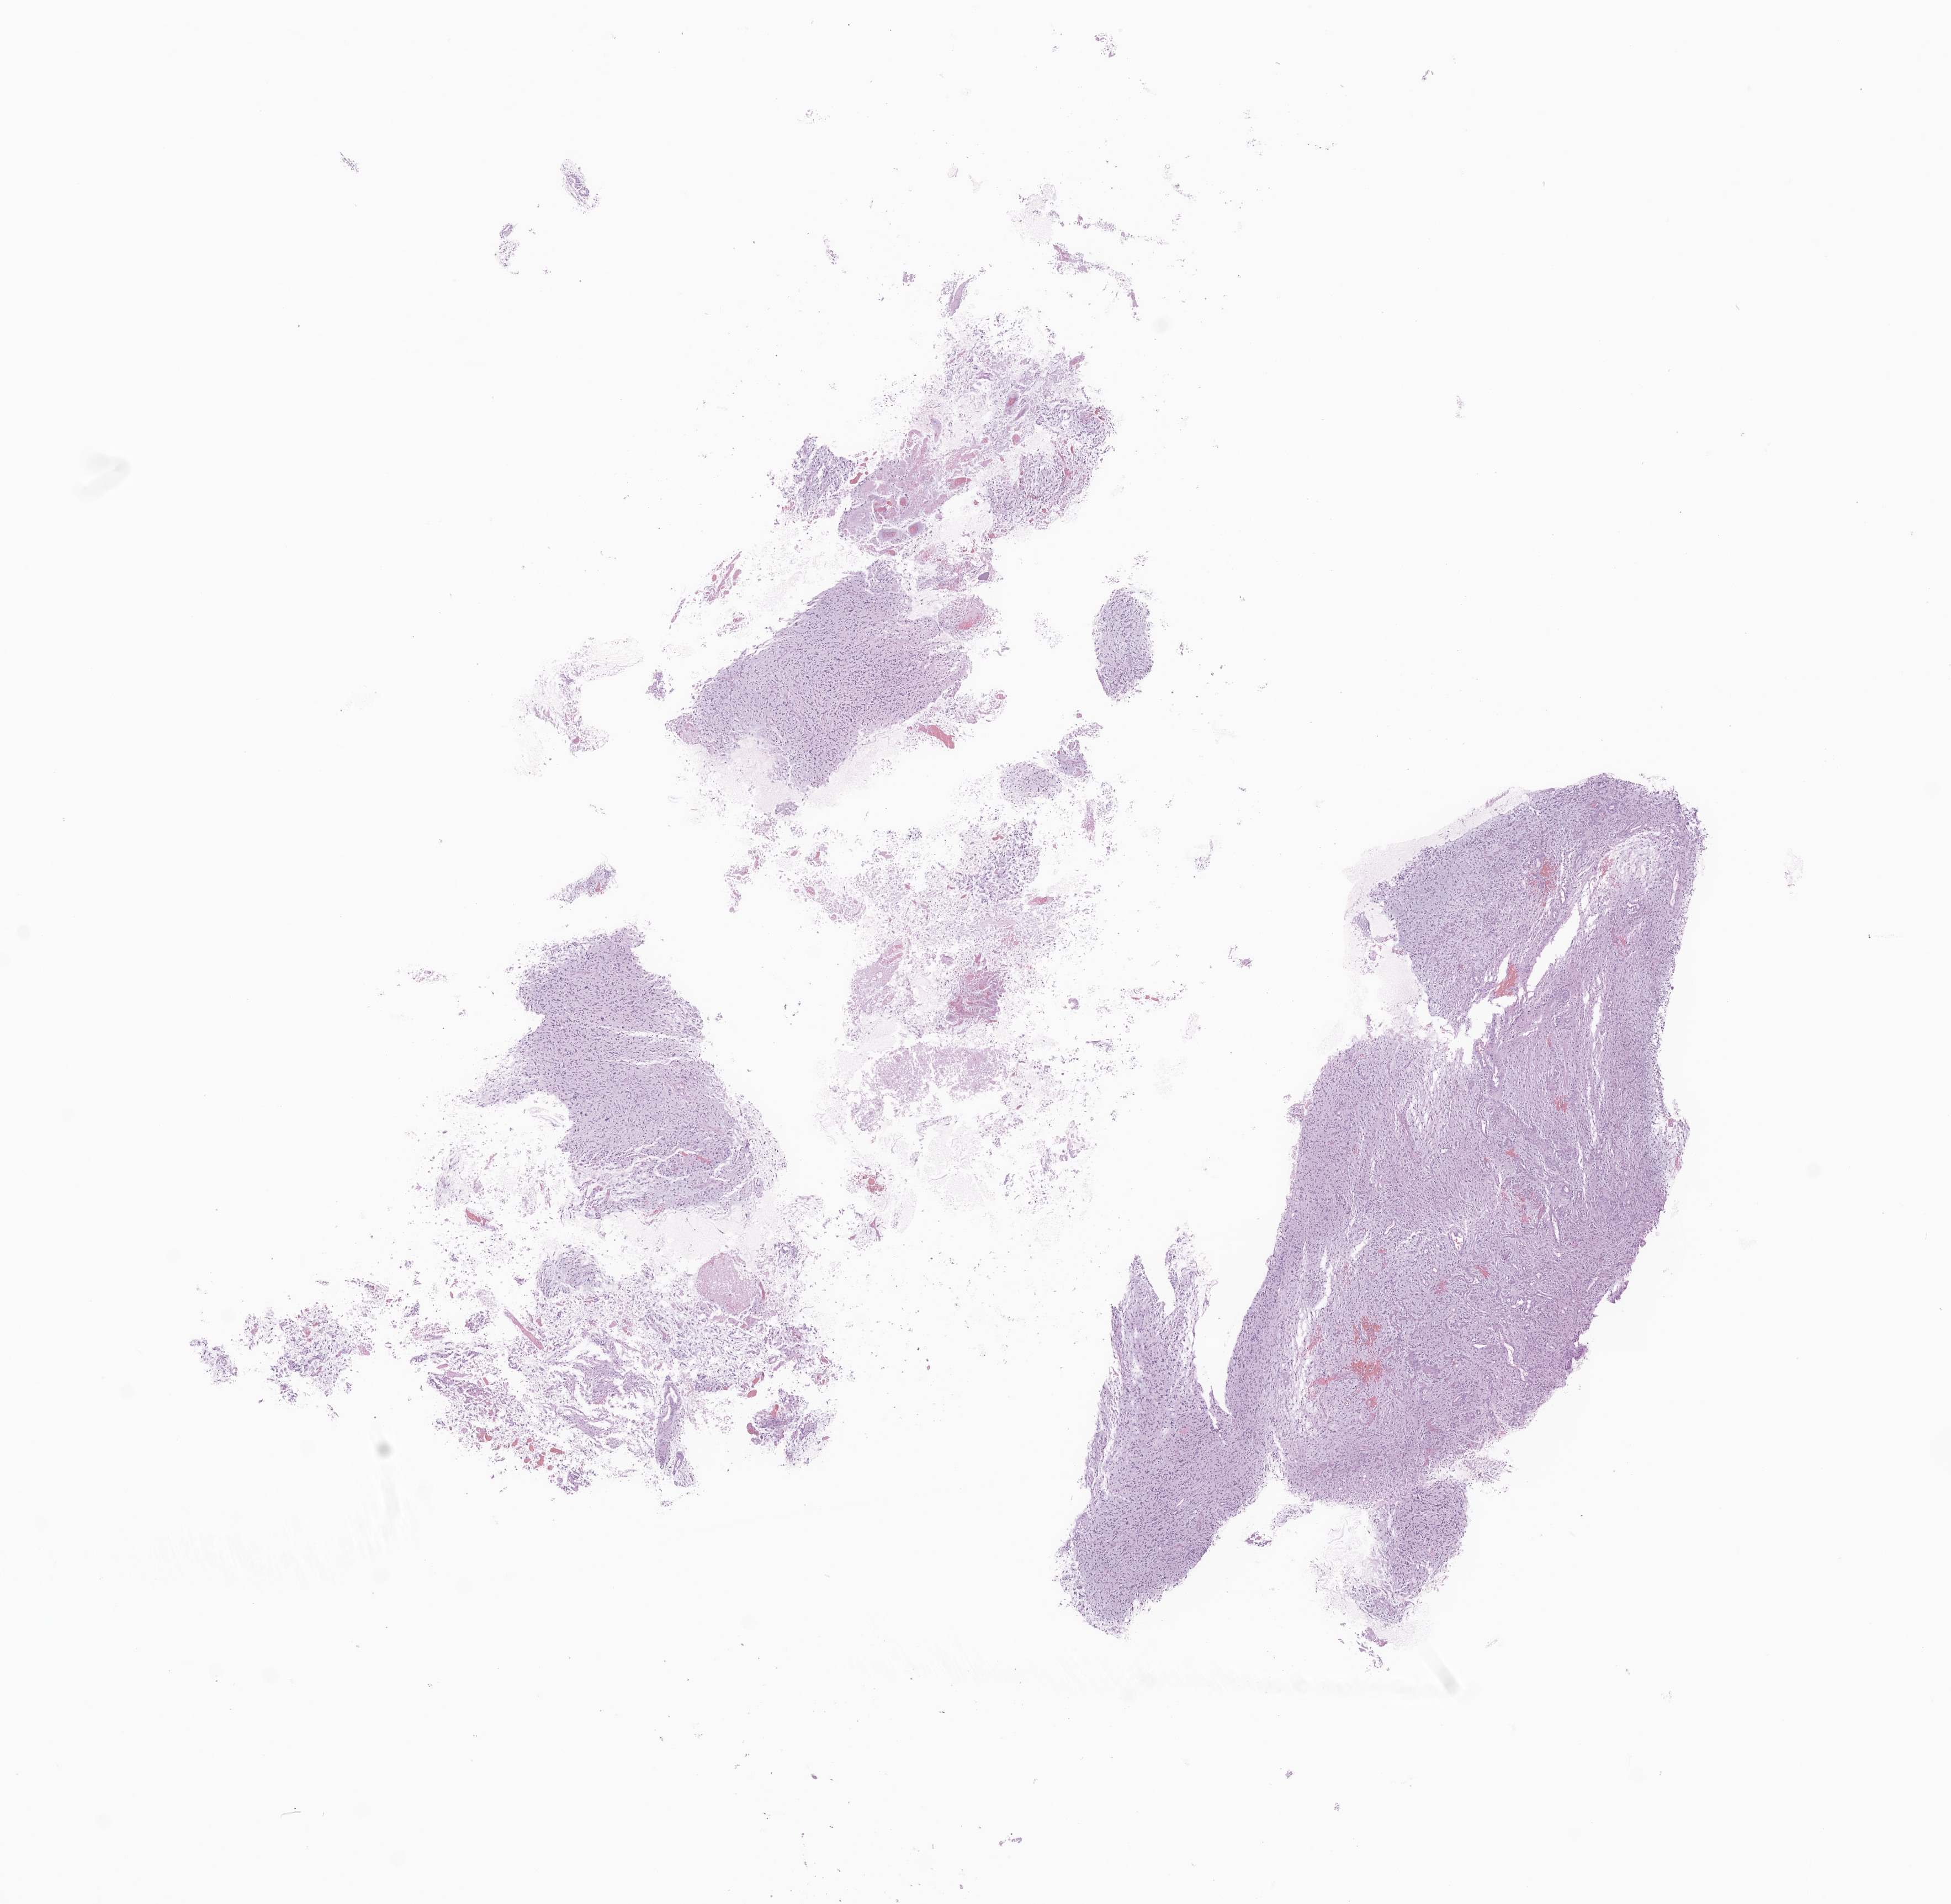
Digitized hematoxylin and eosin (H&E)-stained section of tumor tissue from the brain stem, a low-resolution overview of the entire scanned area, about 14.9 x 14.5 mm; FFPE section. Patient: male, age 180 months (15 years).
* diagnosis (ICD-O-3 morphology term): Glioma, malignant